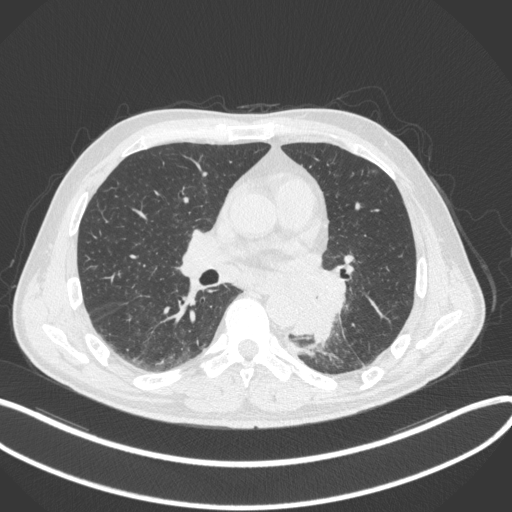
Chest CT, one axial slice; position 173 of 328 along the scan axis; reconstruction kernel B31f; 120 kVp; lung window (W 1500 / L -600 HU); 1 mm slice thickness; 512 × 512 image matrix, field of view 400 × 400 mm. Male patient, age 59 years. From the clinical record (not read from this slice): clinical TNM (as recorded): T2a N2 M0.
Annotated regions visible in this slice (rectangle marked by the reading radiologist):
- lung tumour (recorded histology: squamous cell carcinoma): bounding box <292,271,348,345> (left, top, right, bottom; pixels)